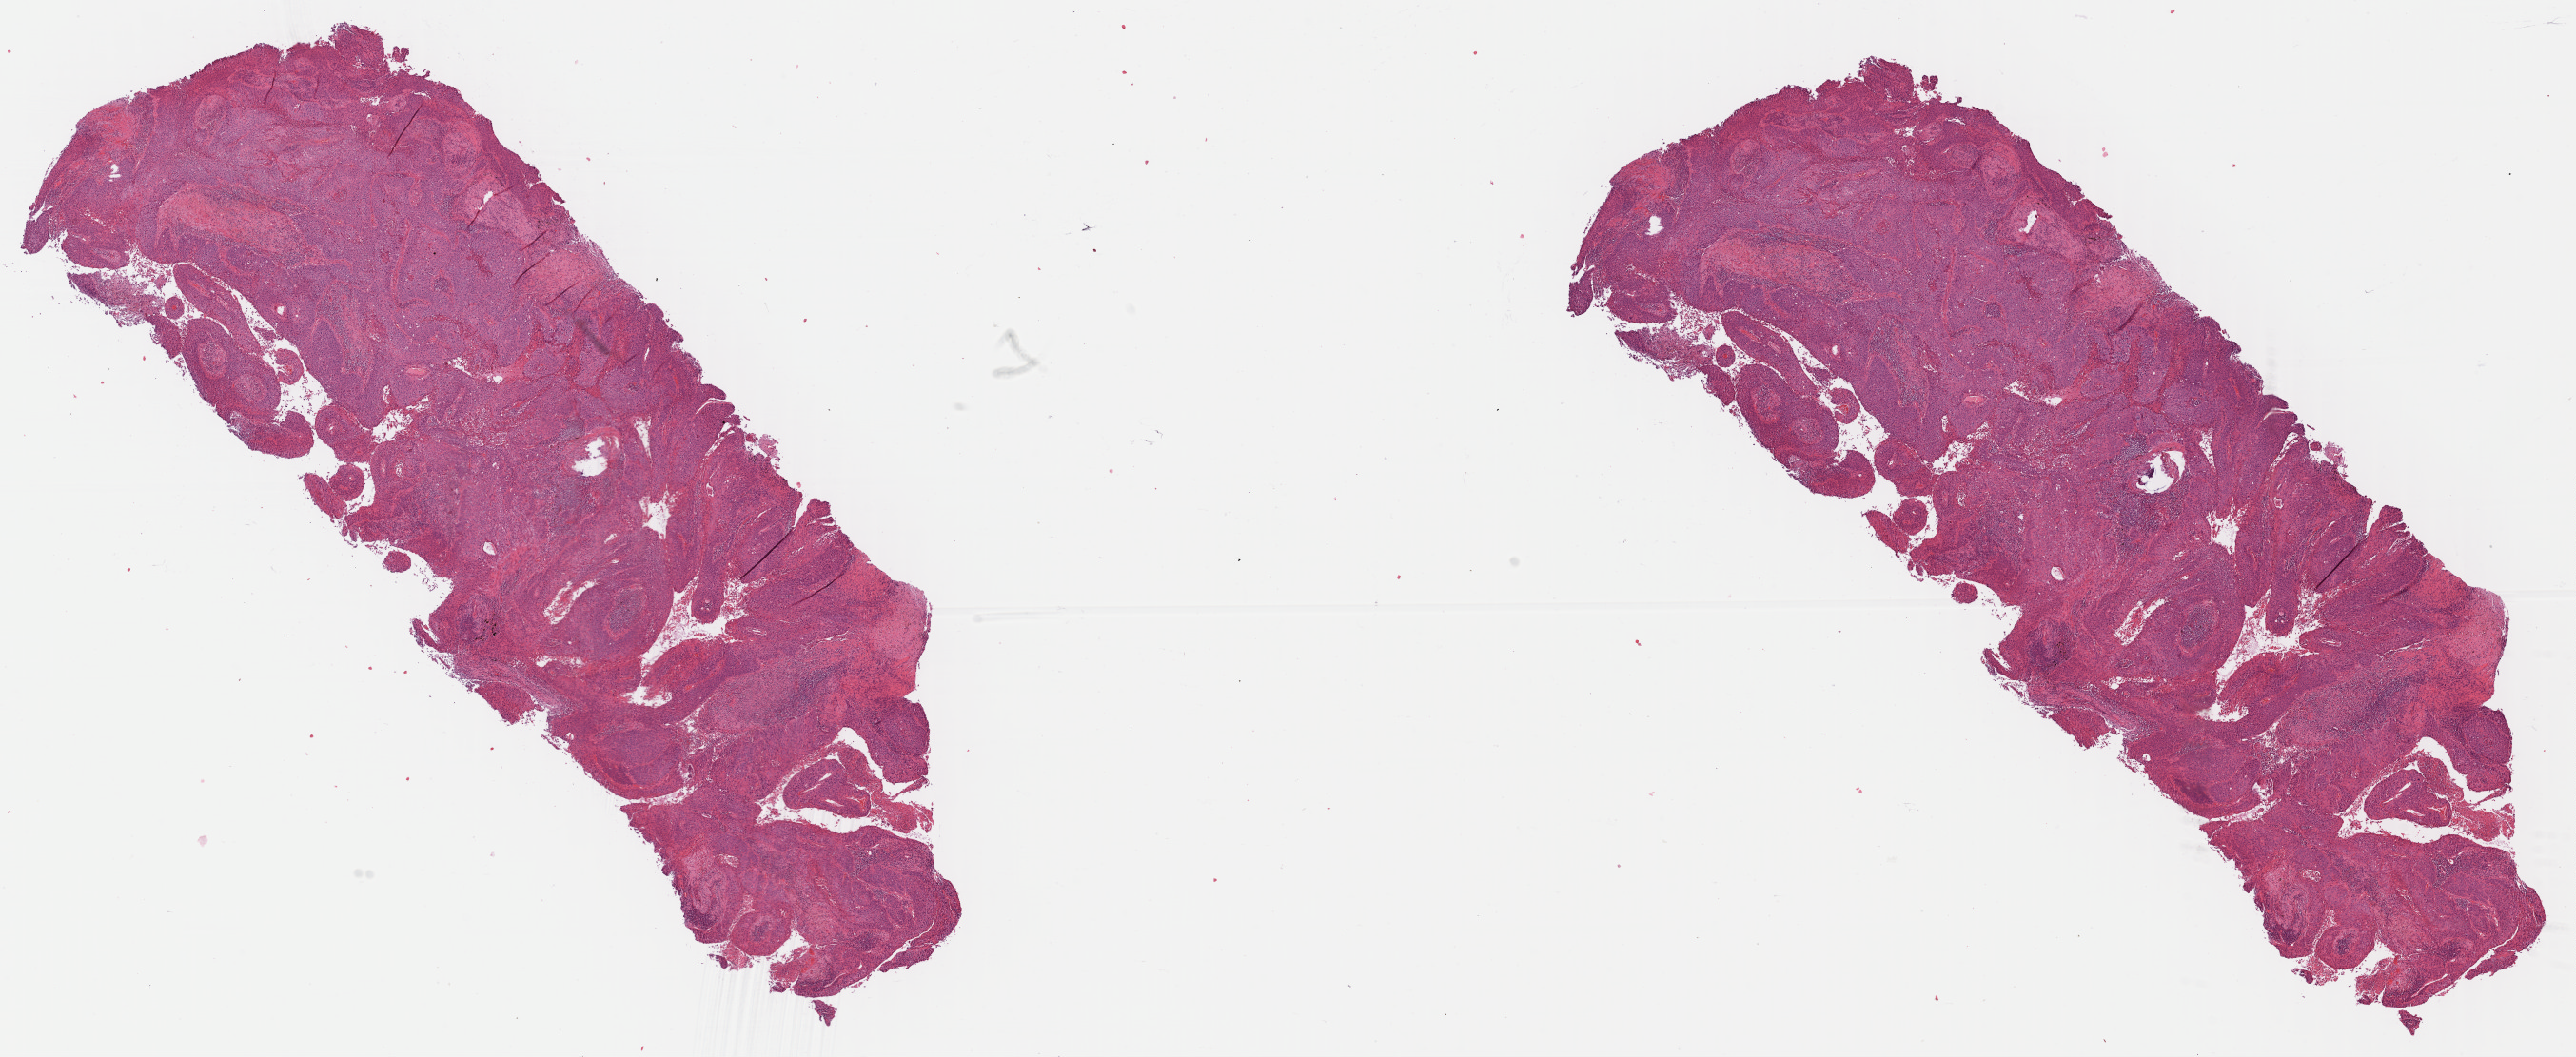
Digitized H&E-stained tissue section (whole slide), whole scanned area (about 21.3 x 8.7 mm, from a 40x scan) shown as a low-resolution overview. Formalin-fixed paraffin-embedded (FFPE) diagnostic section. Lung, primary tumour sample. Male, age 67 years at initial diagnosis.
* AJCC pathologic stage: IIB
* diagnosis: Squamous cell carcinoma, NOS (upper lobe, lung)